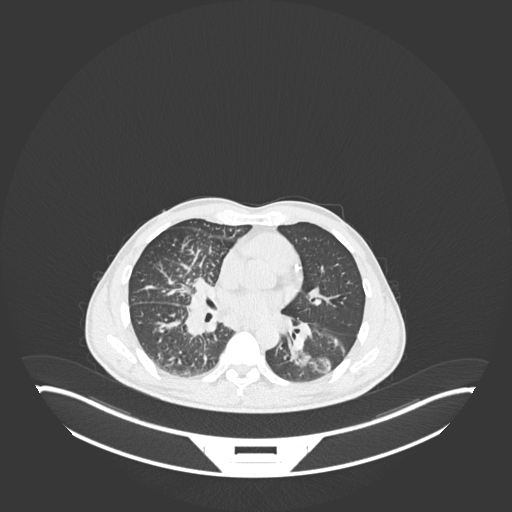
Chest CT, one axial slice; slice 118 of 237 in the series (ordered by position); reconstruction kernel B30f; 120 kVp; lung window (W 1500 / L -600 HU); 512 × 512 image matrix. Male patient, age 49 years. Case-level facts recorded for this patient, not image findings: clinical TNM (as recorded): T2b N1 M0.
Annotated regions visible in this slice (rectangle marked by the reading radiologist):
- lung tumour (recorded histology: adenocarcinoma): bounding box (x1, y1, x2, y2) in pixels: (290, 315, 353, 378)